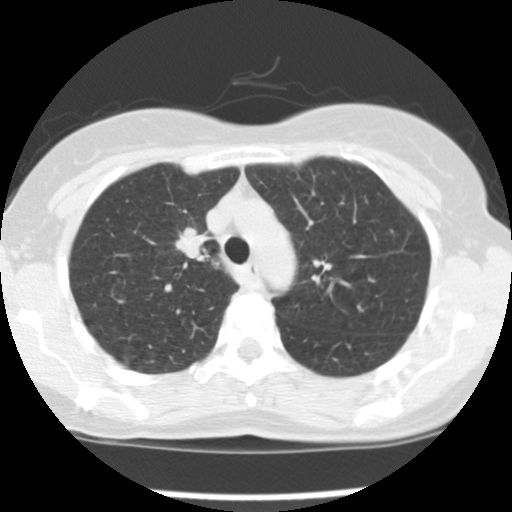
Low-dose screening chest CT, one axial slice; position 116 of 157 along the scan axis; reconstruction kernel STANDARD; 120 kVp; lung window (W 1500 / L -600 HU); 2.5 mm slice thickness; 512 × 512 image matrix, field of view 282 × 282 mm.
Outlined on this slice (outlined manually by an expert reader):
- lesion 1 (tumor, upper lobe of right lung): box from (x=176, y=227) to (x=210, y=259) px